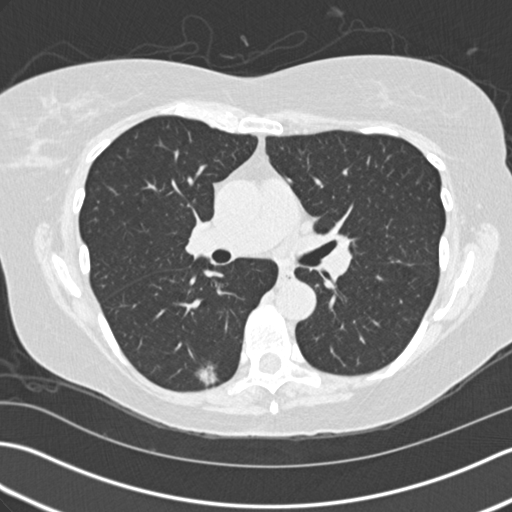
Chest CT (low-dose screening protocol), one axial image. Third screening round (two years after baseline). Lung window (W 1500 / L -600 HU). 2 mm slice thickness. Standard (soft-tissue) reconstruction kernel (B30f). Slice 72 of 159 in the series. Female participant, aged 60 years at enrolment. Former smoker at enrolment.
• Expert-annotated lung lesion, box from (x=184, y=350) to (x=232, y=392) px.
• The screening reader recorded 3 non-calcified nodules or masses ≥4 mm on this exam (right lower lobe, right middle lobe, right middle lobe); which of them this box marks is not recorded.
• Participant outcome: lung cancer diagnosed 68 days after this screen — acinar cell carcinoma, right lower lobe, moderately differentiated (G2), stage IA (AJCC 6th edition), 10 mm at pathology.